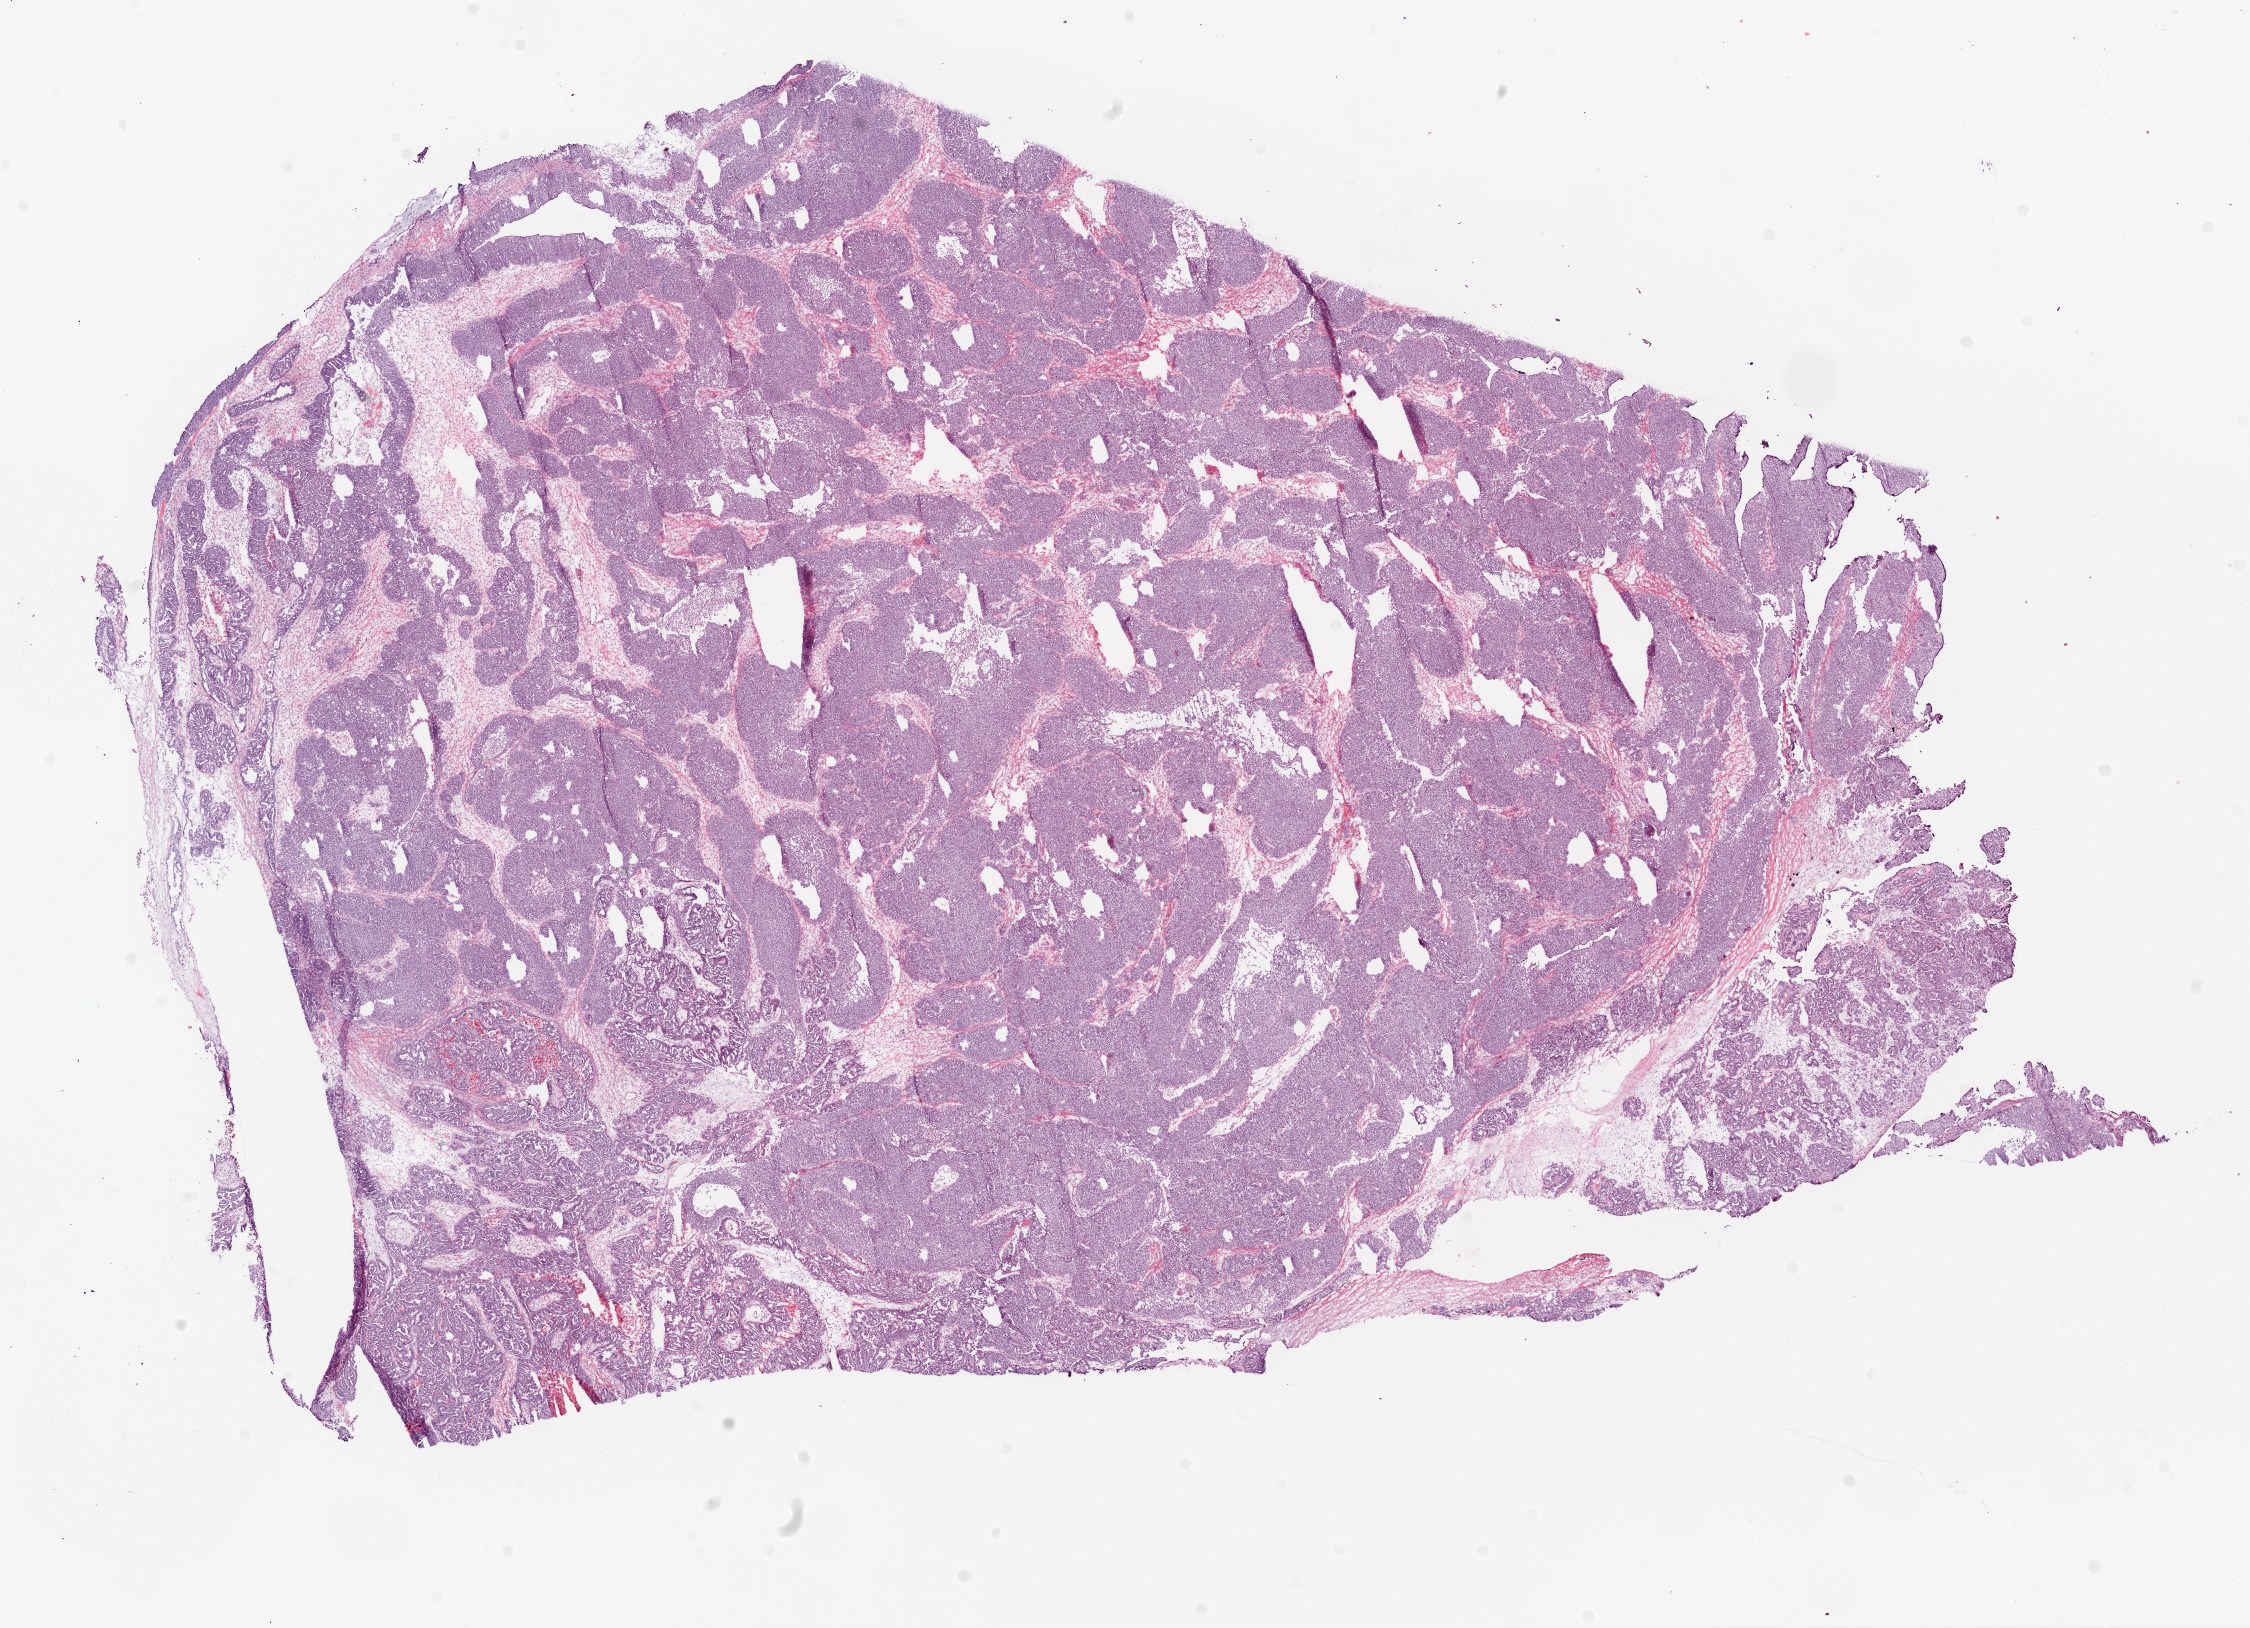
Hematoxylin and eosin (H&E) stained whole-slide image — shown as a low-resolution overview of the whole scanned area (about 18.1 x 13.1 mm, slide scanned at 20x). Frozen section from the top of the tissue portion. Ovary, primary tumour sample. Female, age 57 years at initial diagnosis. Histologic grade: G3 (poorly differentiated). Pathologist review of this section (percent, as recorded): tumour cells 89%, tumour nuclei 90%, normal cells 0%, stromal cells 10%, necrosis 1%.
Histologic diagnosis: Serous cystadenocarcinoma, NOS. FIGO stage: IIIC. Laterality: bilateral.